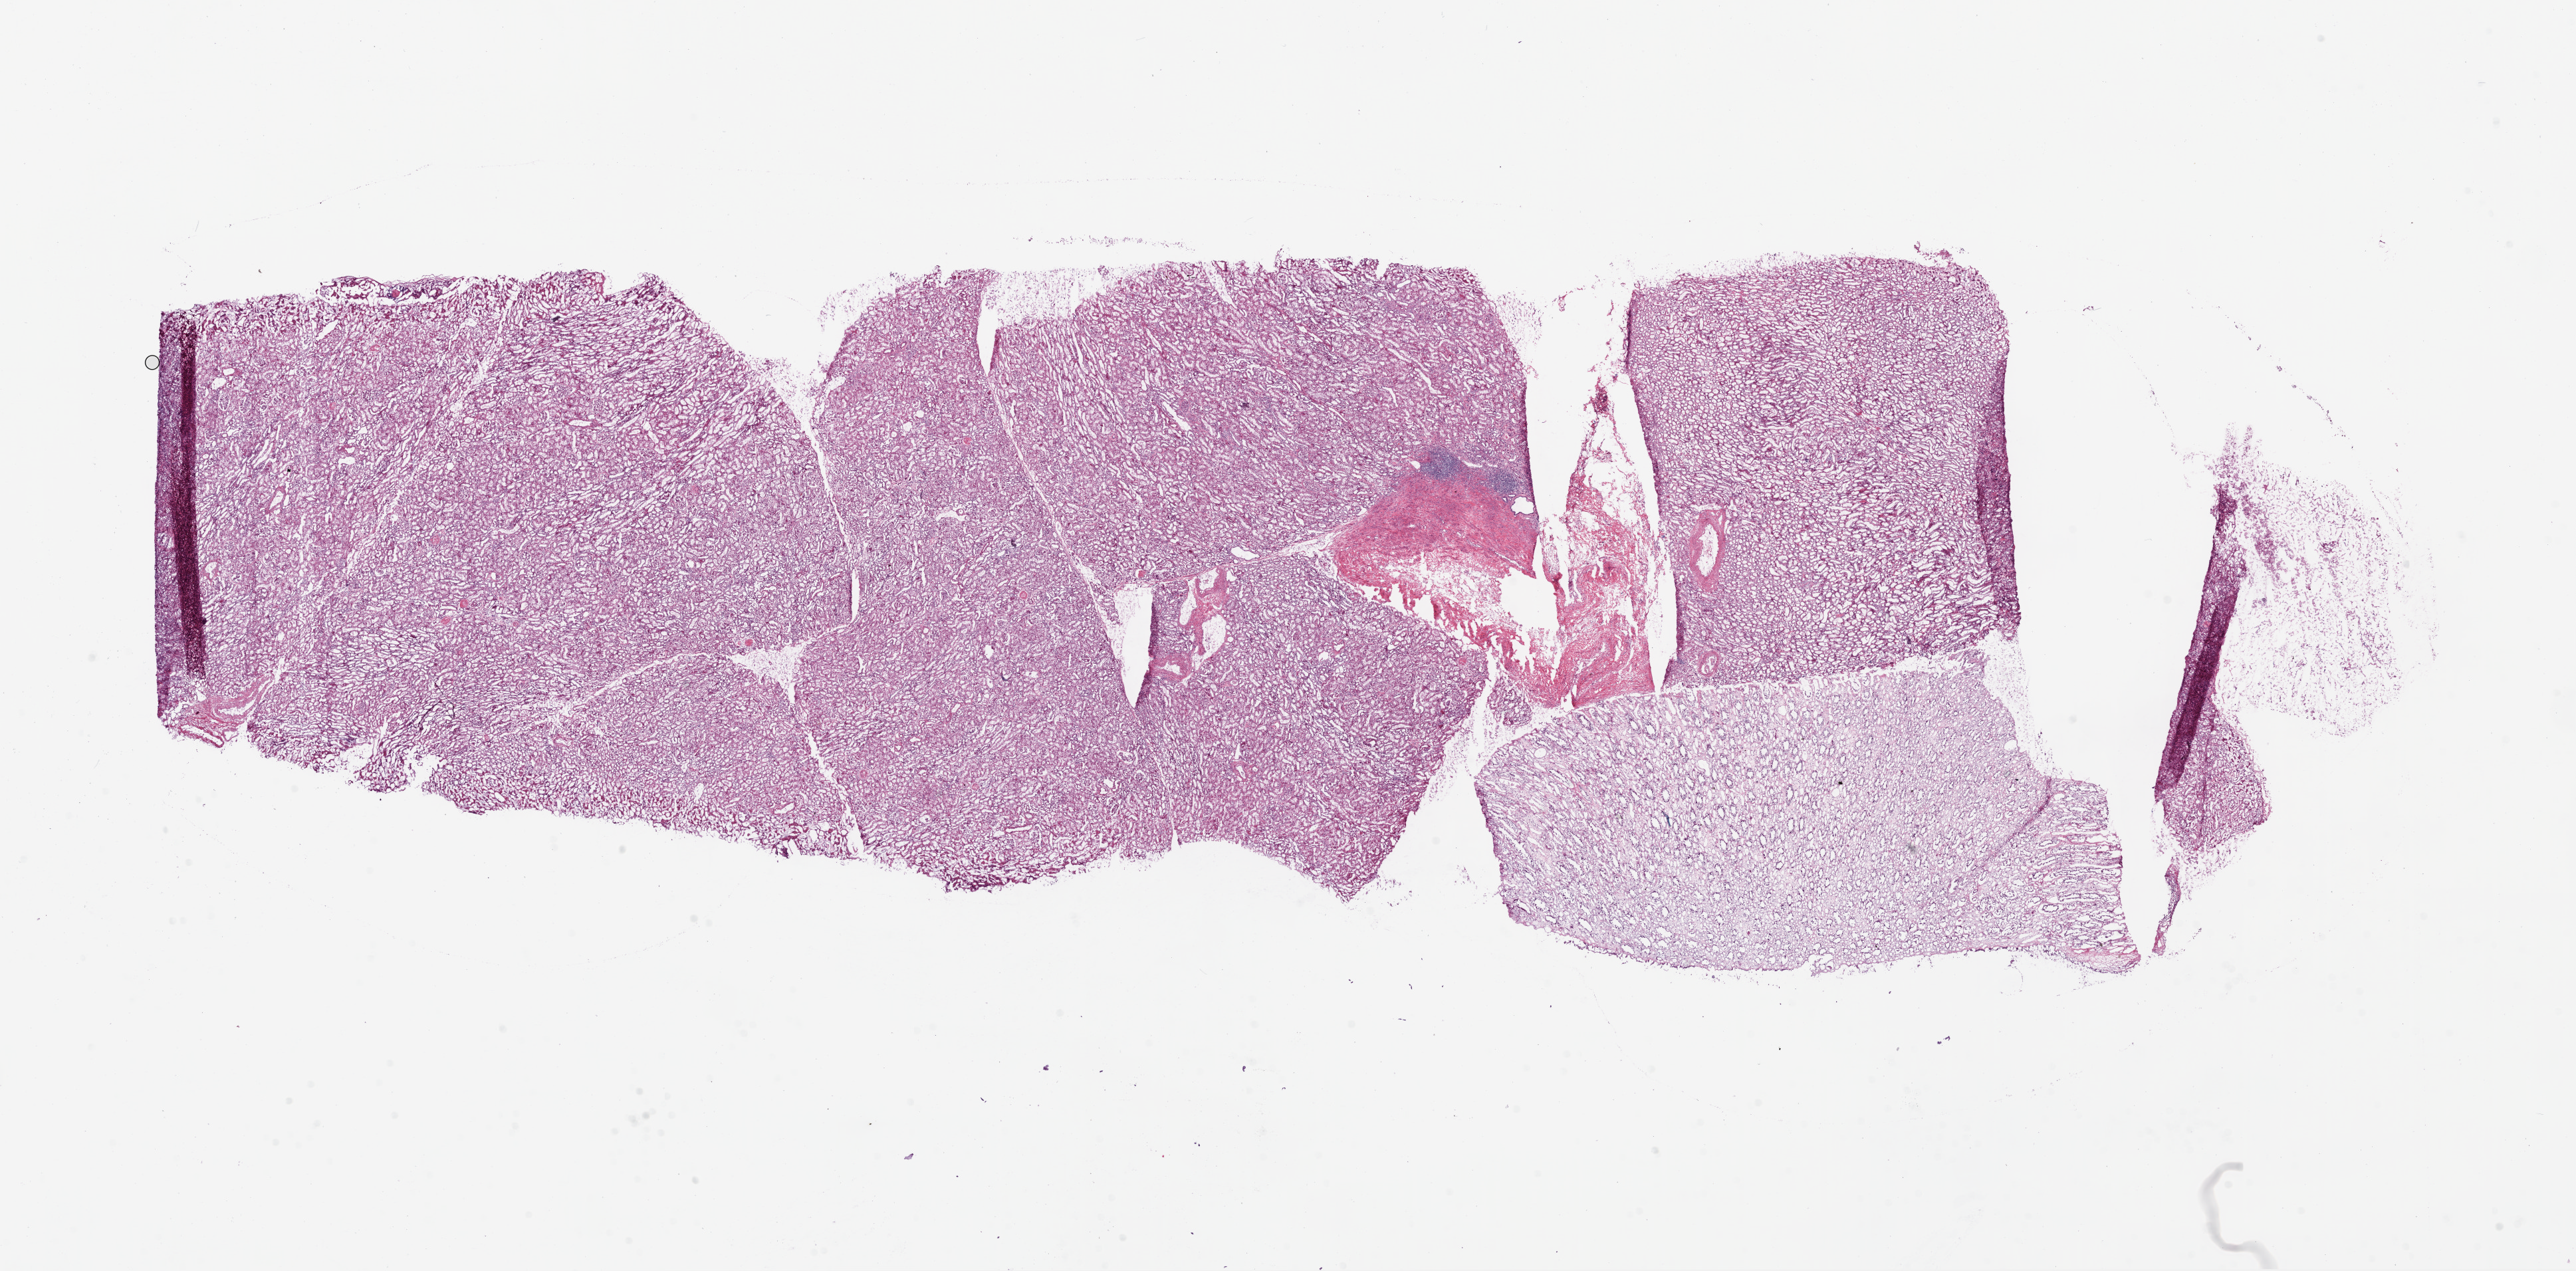
Whole-slide histology image, H&E-stained — low-resolution overview of the scanned area, about 31.1 x 15.3 mm, frozen section from the bottom of the tissue portion, kidney, solid tissue normal (non-tumour tissue) sample. Patient: female, age at initial diagnosis 60 years.
- this section: solid tissue normal sample (biorepository sample class)
- patient diagnosis: Clear cell adenocarcinoma, NOS